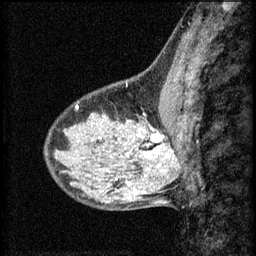
Breast MRI (dynamic contrast-enhanced), one sagittal slice; position 20 of 60 along the scan axis; 3 images stored at this slice position (order not interpretable as contrast timing); 1.5 T; TE 4.2 ms, TR 8.2 ms; 256 × 256 image matrix, field of view 180 × 180 mm. Patient: female, 40 years.
Structures marked on this image (semi-automatically segmented with operator editing):
- analysis volume of interest (the breast-tissue region the enhancement analysis was run in; not a lesion): bounding box <108,108,167,159> (left, top, right, bottom; pixels)
- tumour enhancement mask (voxels above the 70 % enhancement threshold inside the analysis volume of interest): <140,128,163,153>